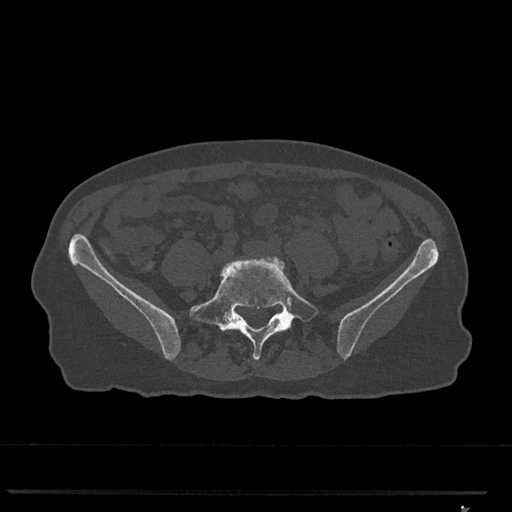
CT including the spine, one axial slice. Position 155 of 793 along the scan axis. Reconstruction kernel Br40s/3. Bone window (W 1800 / L 400 HU). 0.5 mm slice thickness. 512 × 512 image matrix, field of view 380 × 380 mm. Patient: female, 62 years. Case-level facts recorded for this patient, not image findings: primary cancer: renal.
Annotated regions visible in this slice (semi-automatic segmentation, software-assisted and operator-edited):
- L4 vertebra: bounding box (x1, y1, x2, y2) in pixels: (220, 267, 224, 274)
- L5 vertebra: (190, 257, 318, 360)